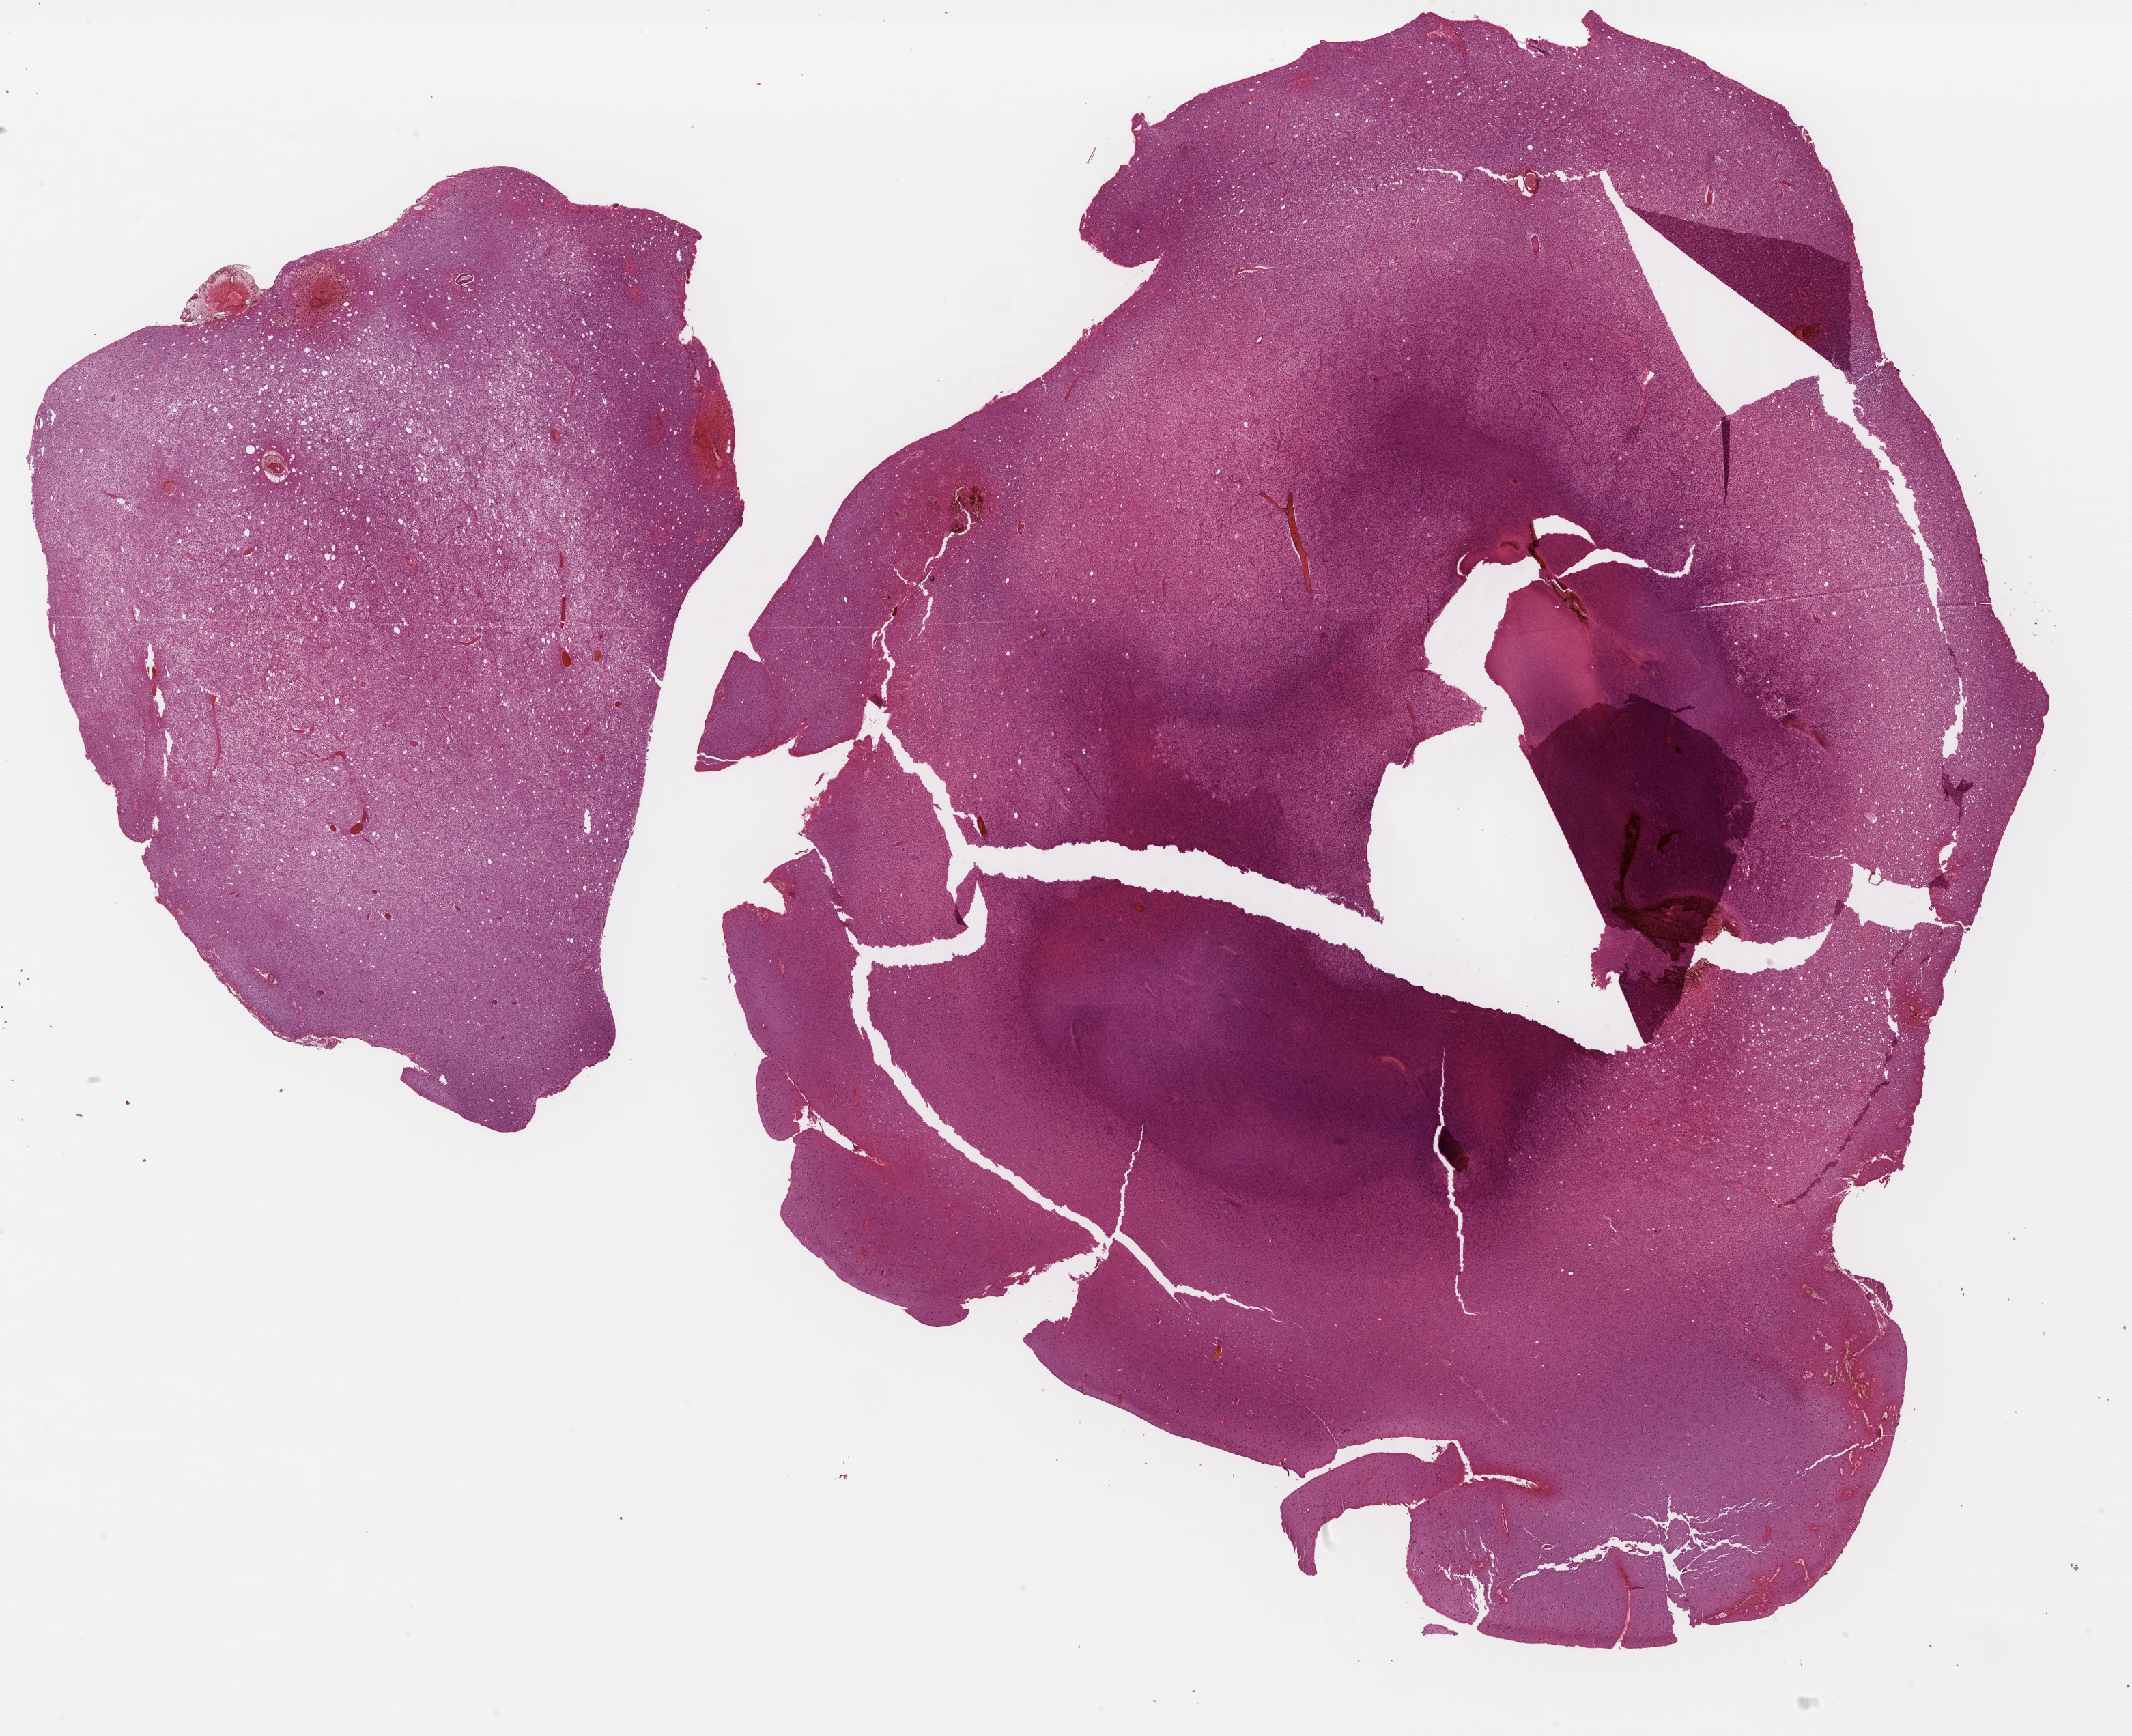
Whole-slide histology image, H&E-stained — a low-resolution overview of the entire scanned area, about 24.6 x 20.0 mm (acquisition: 40x scan), formalin-fixed paraffin-embedded (FFPE) diagnostic section, primary tumour sample from the brain. Patient: female, age at initial diagnosis 20 years. Histologic grade: G2 (moderately differentiated).
Pathologic diagnosis: Oligodendroglioma, NOS.